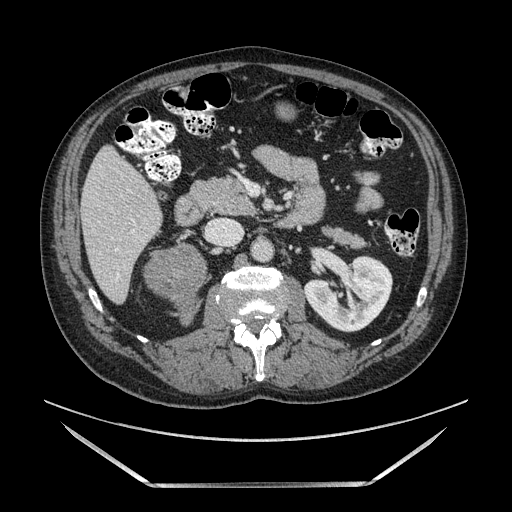
Contrast-enhanced abdominal CT, one axial slice. Position 54 of 185 along the scan axis. Soft-tissue window (W 400 / L 40 HU). 1.25 mm slice thickness. 512 × 512 image matrix. Male patient. From the clinical record (not read from this slice): diagnosis: adrenocortical carcinoma; tumour side: right adrenal; tumour size at pathology: 10.3 cm.
Annotated regions visible in this slice (semi-automatic segmentation, software-assisted and operator-edited):
- mass: bounding box <143,245,208,322> (left, top, right, bottom; pixels)